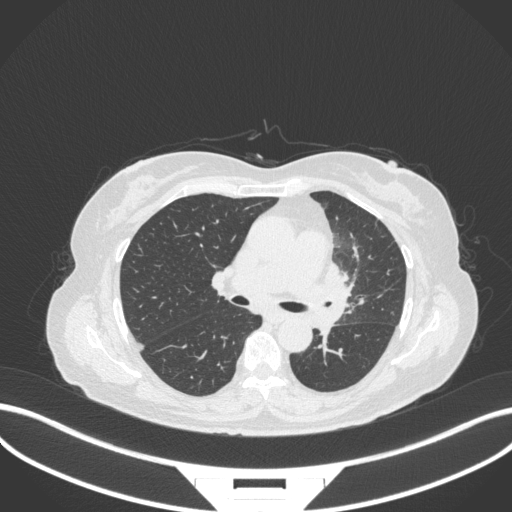
Chest CT, one axial slice; position 197 of 382 along the scan axis; reconstruction kernel B31f; 120 kVp; lung window (W 1500 / L -600 HU); 1 mm slice thickness; 512 × 512 image matrix. Female patient, age 64 years. From the clinical record (not read from this slice): clinical TNM (as recorded): T2a N2 M0.
Outlined on this slice (bounding box drawn by a radiologist):
- lung tumour (recorded histology: adenocarcinoma): bounding box (x1, y1, x2, y2) in pixels: (323, 259, 352, 342)